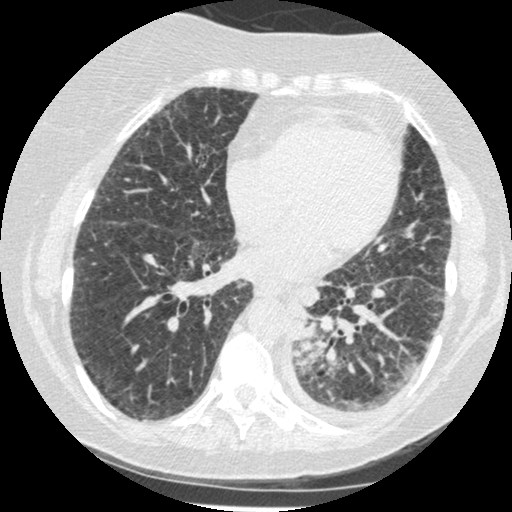
Chest CT (low-dose screening protocol), one axial image; third screening round (two years after baseline); lung window (W 1500 / L -600 HU); 512 × 512 image matrix. Female, age 60 years at enrolment. Former smoker at enrolment.
Expert reader's lesion annotation, bounding box <279,301,343,377> (left, top, right, bottom; pixels). Screening reader's record for this exam (one nodule recorded; not confirmed to be the boxed lesion): non-calcified nodule or mass ≥4 mm, left lower lobe, 54 × 38 mm, smooth margins, soft tissue attenuation, pre-existing on the prior screen: yes; interval growth: yes. Official screen result: positive, other. Participant outcome: lung cancer diagnosed 15 days after this screen — small cell carcinoma, NOS, left lower lobe, undifferentiated (G4), stage IV (AJCC 6th edition), 69 mm at pathology.